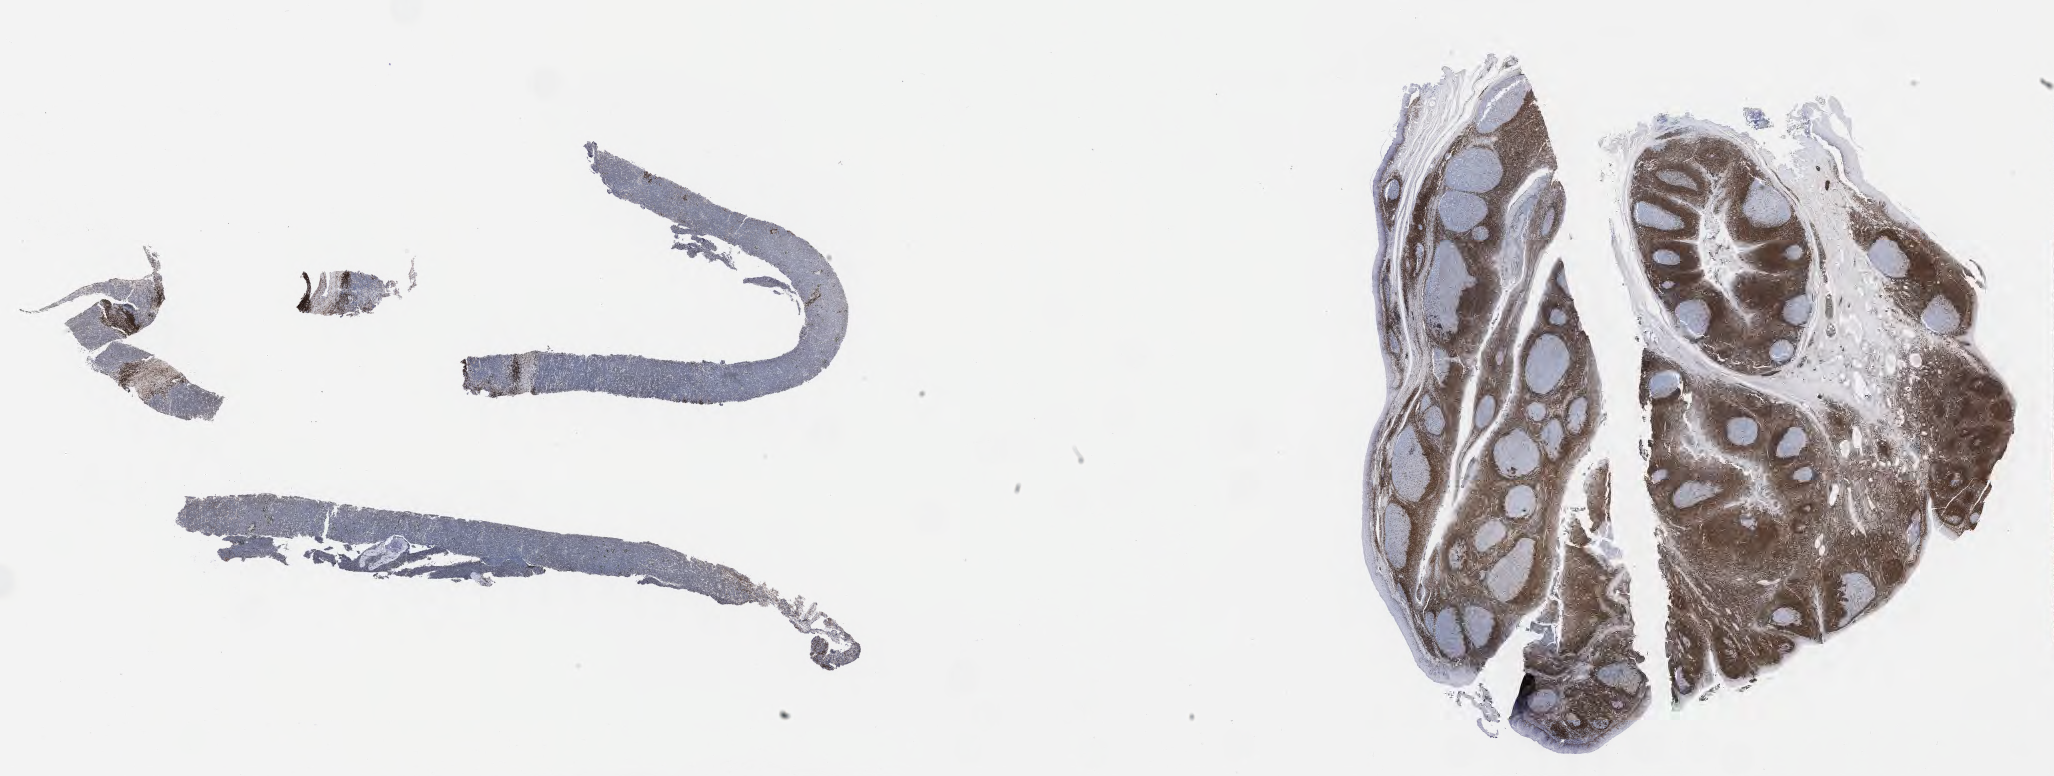
IHC for BCL2, whole-slide image — shown as a low-resolution overview of the whole scanned area (about 33.2 x 12.5 mm), specimen: tumor tissue. Patient male; 55 years old.
Histologic diagnosis: Burkitt lymphoma, NOS.